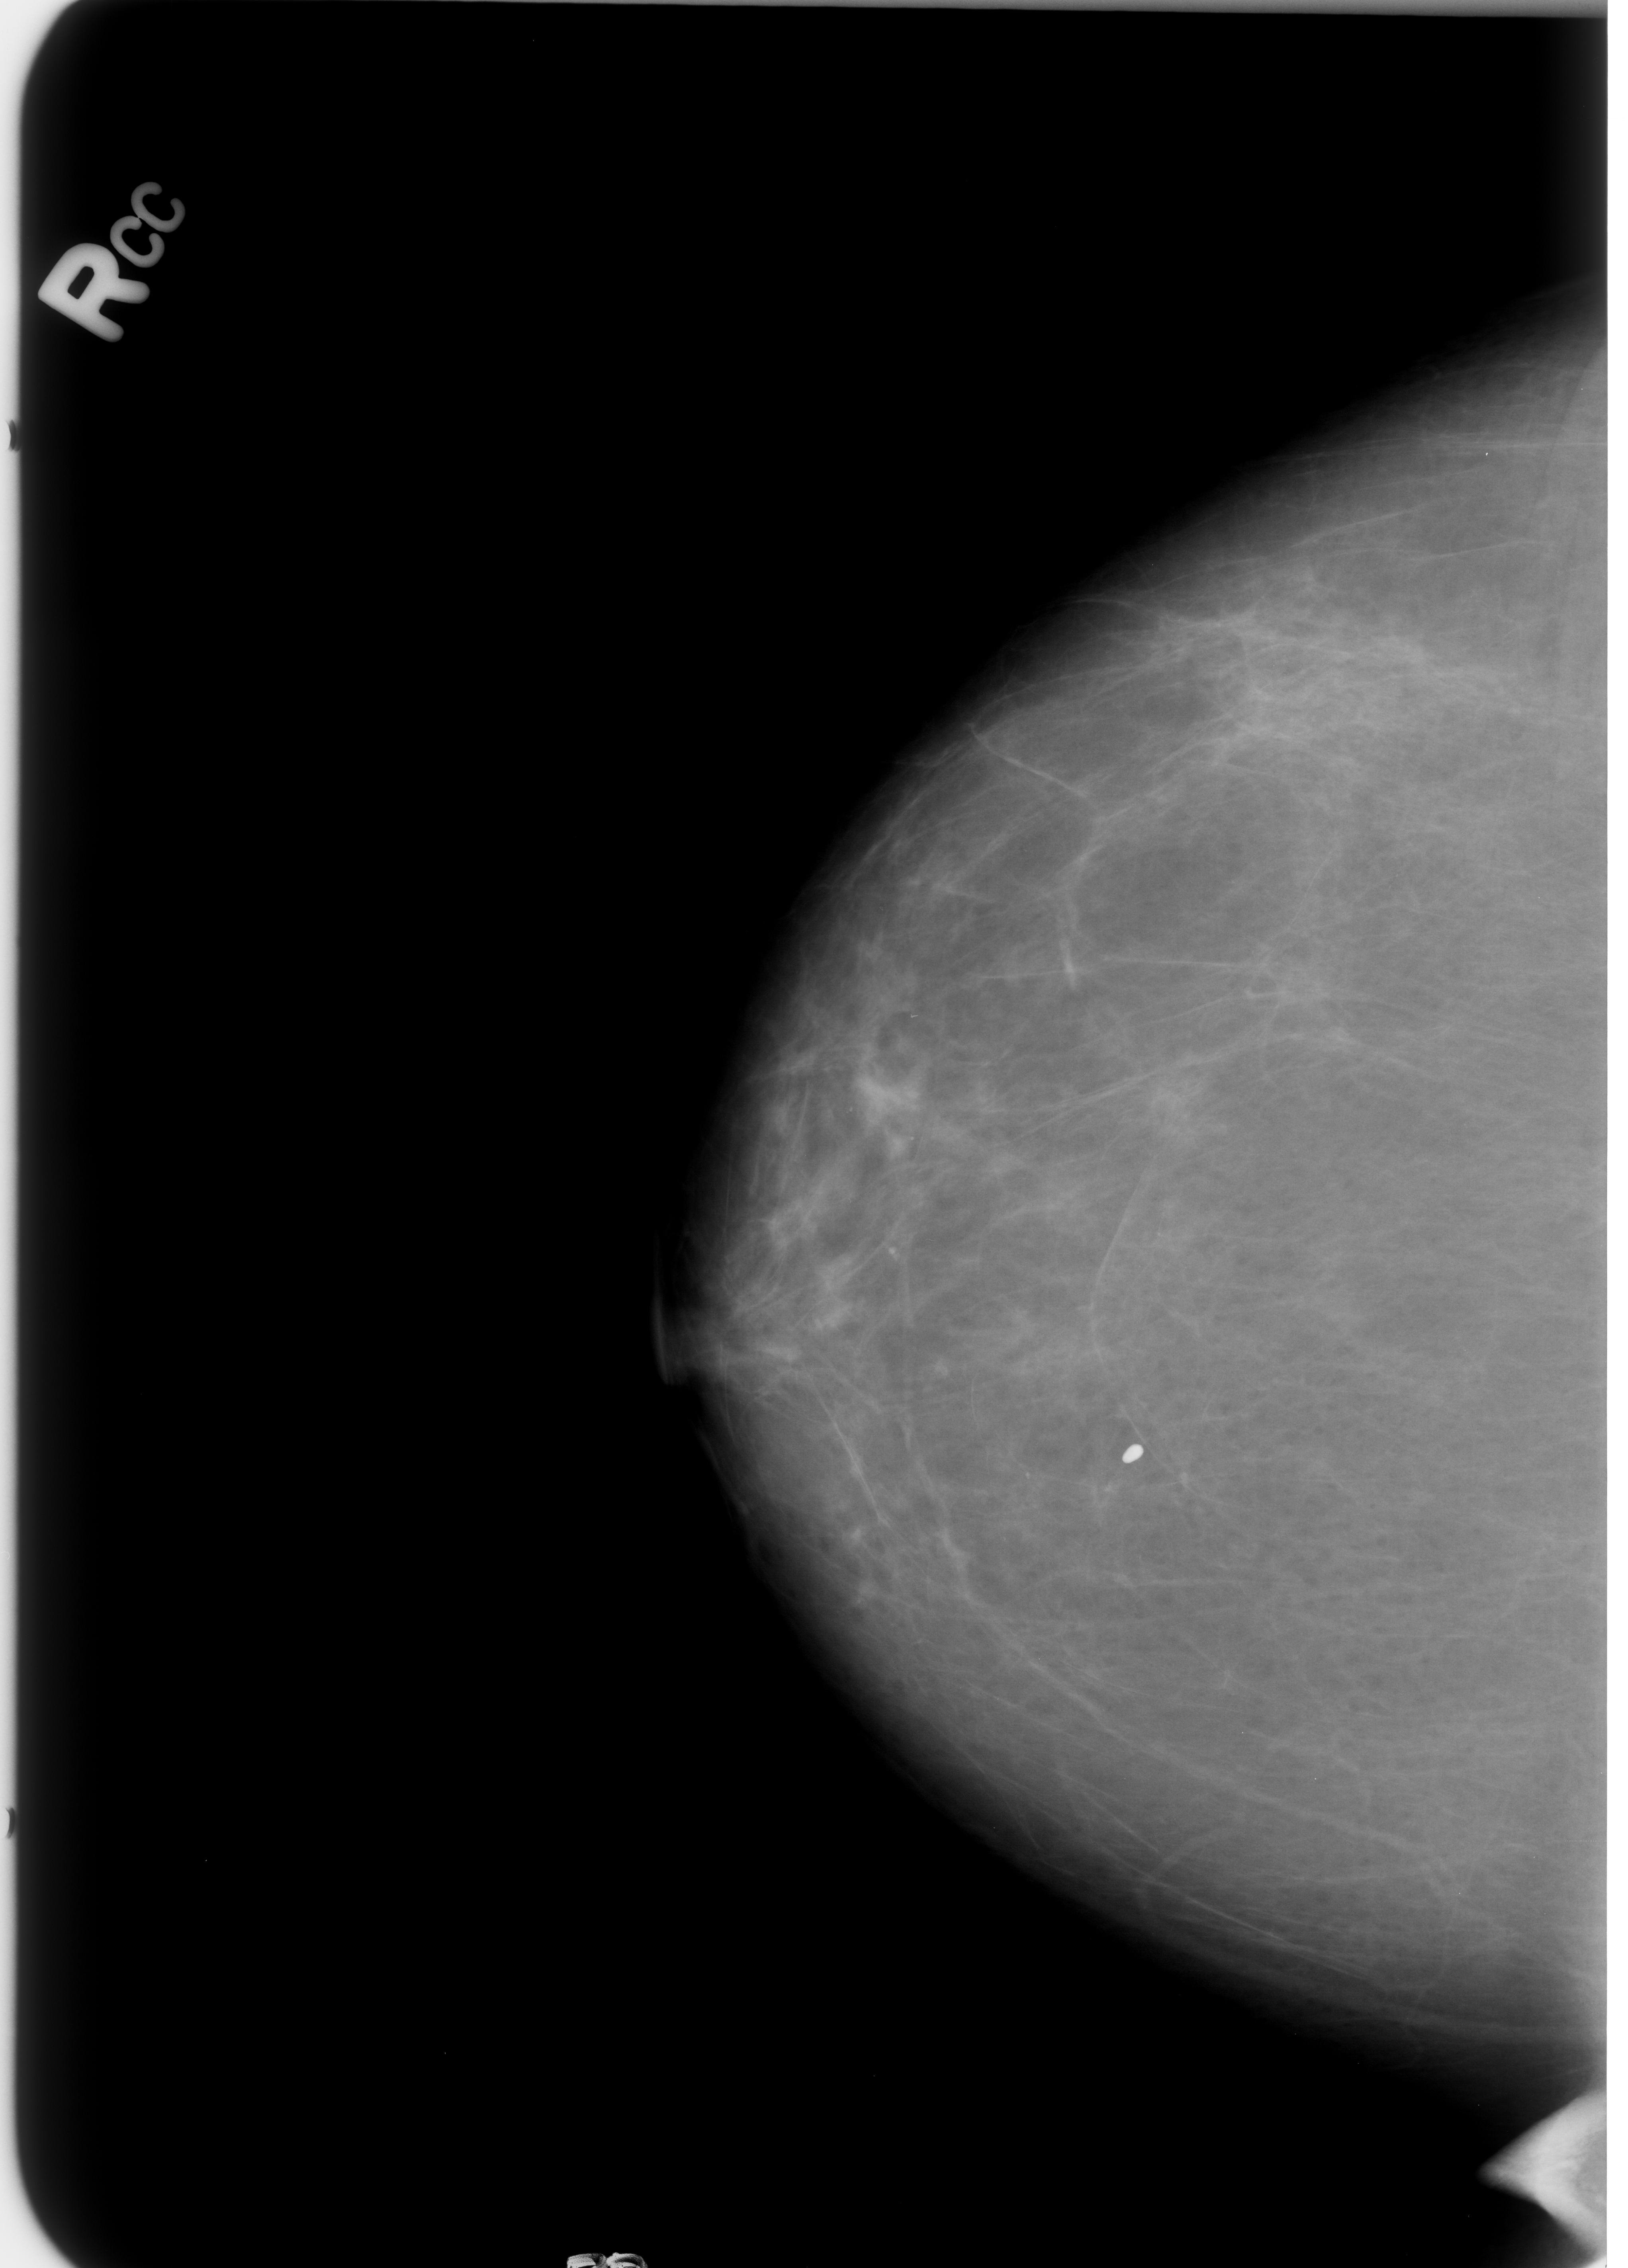
Mammogram (digitized film); right breast; craniocaudal (CC) view; BI-RADS breast density category 1 (scale 1–4).
Marked abnormality: calcifications, morphology coarse; BI-RADS assessment category 2; benign without callback (not worked up further).